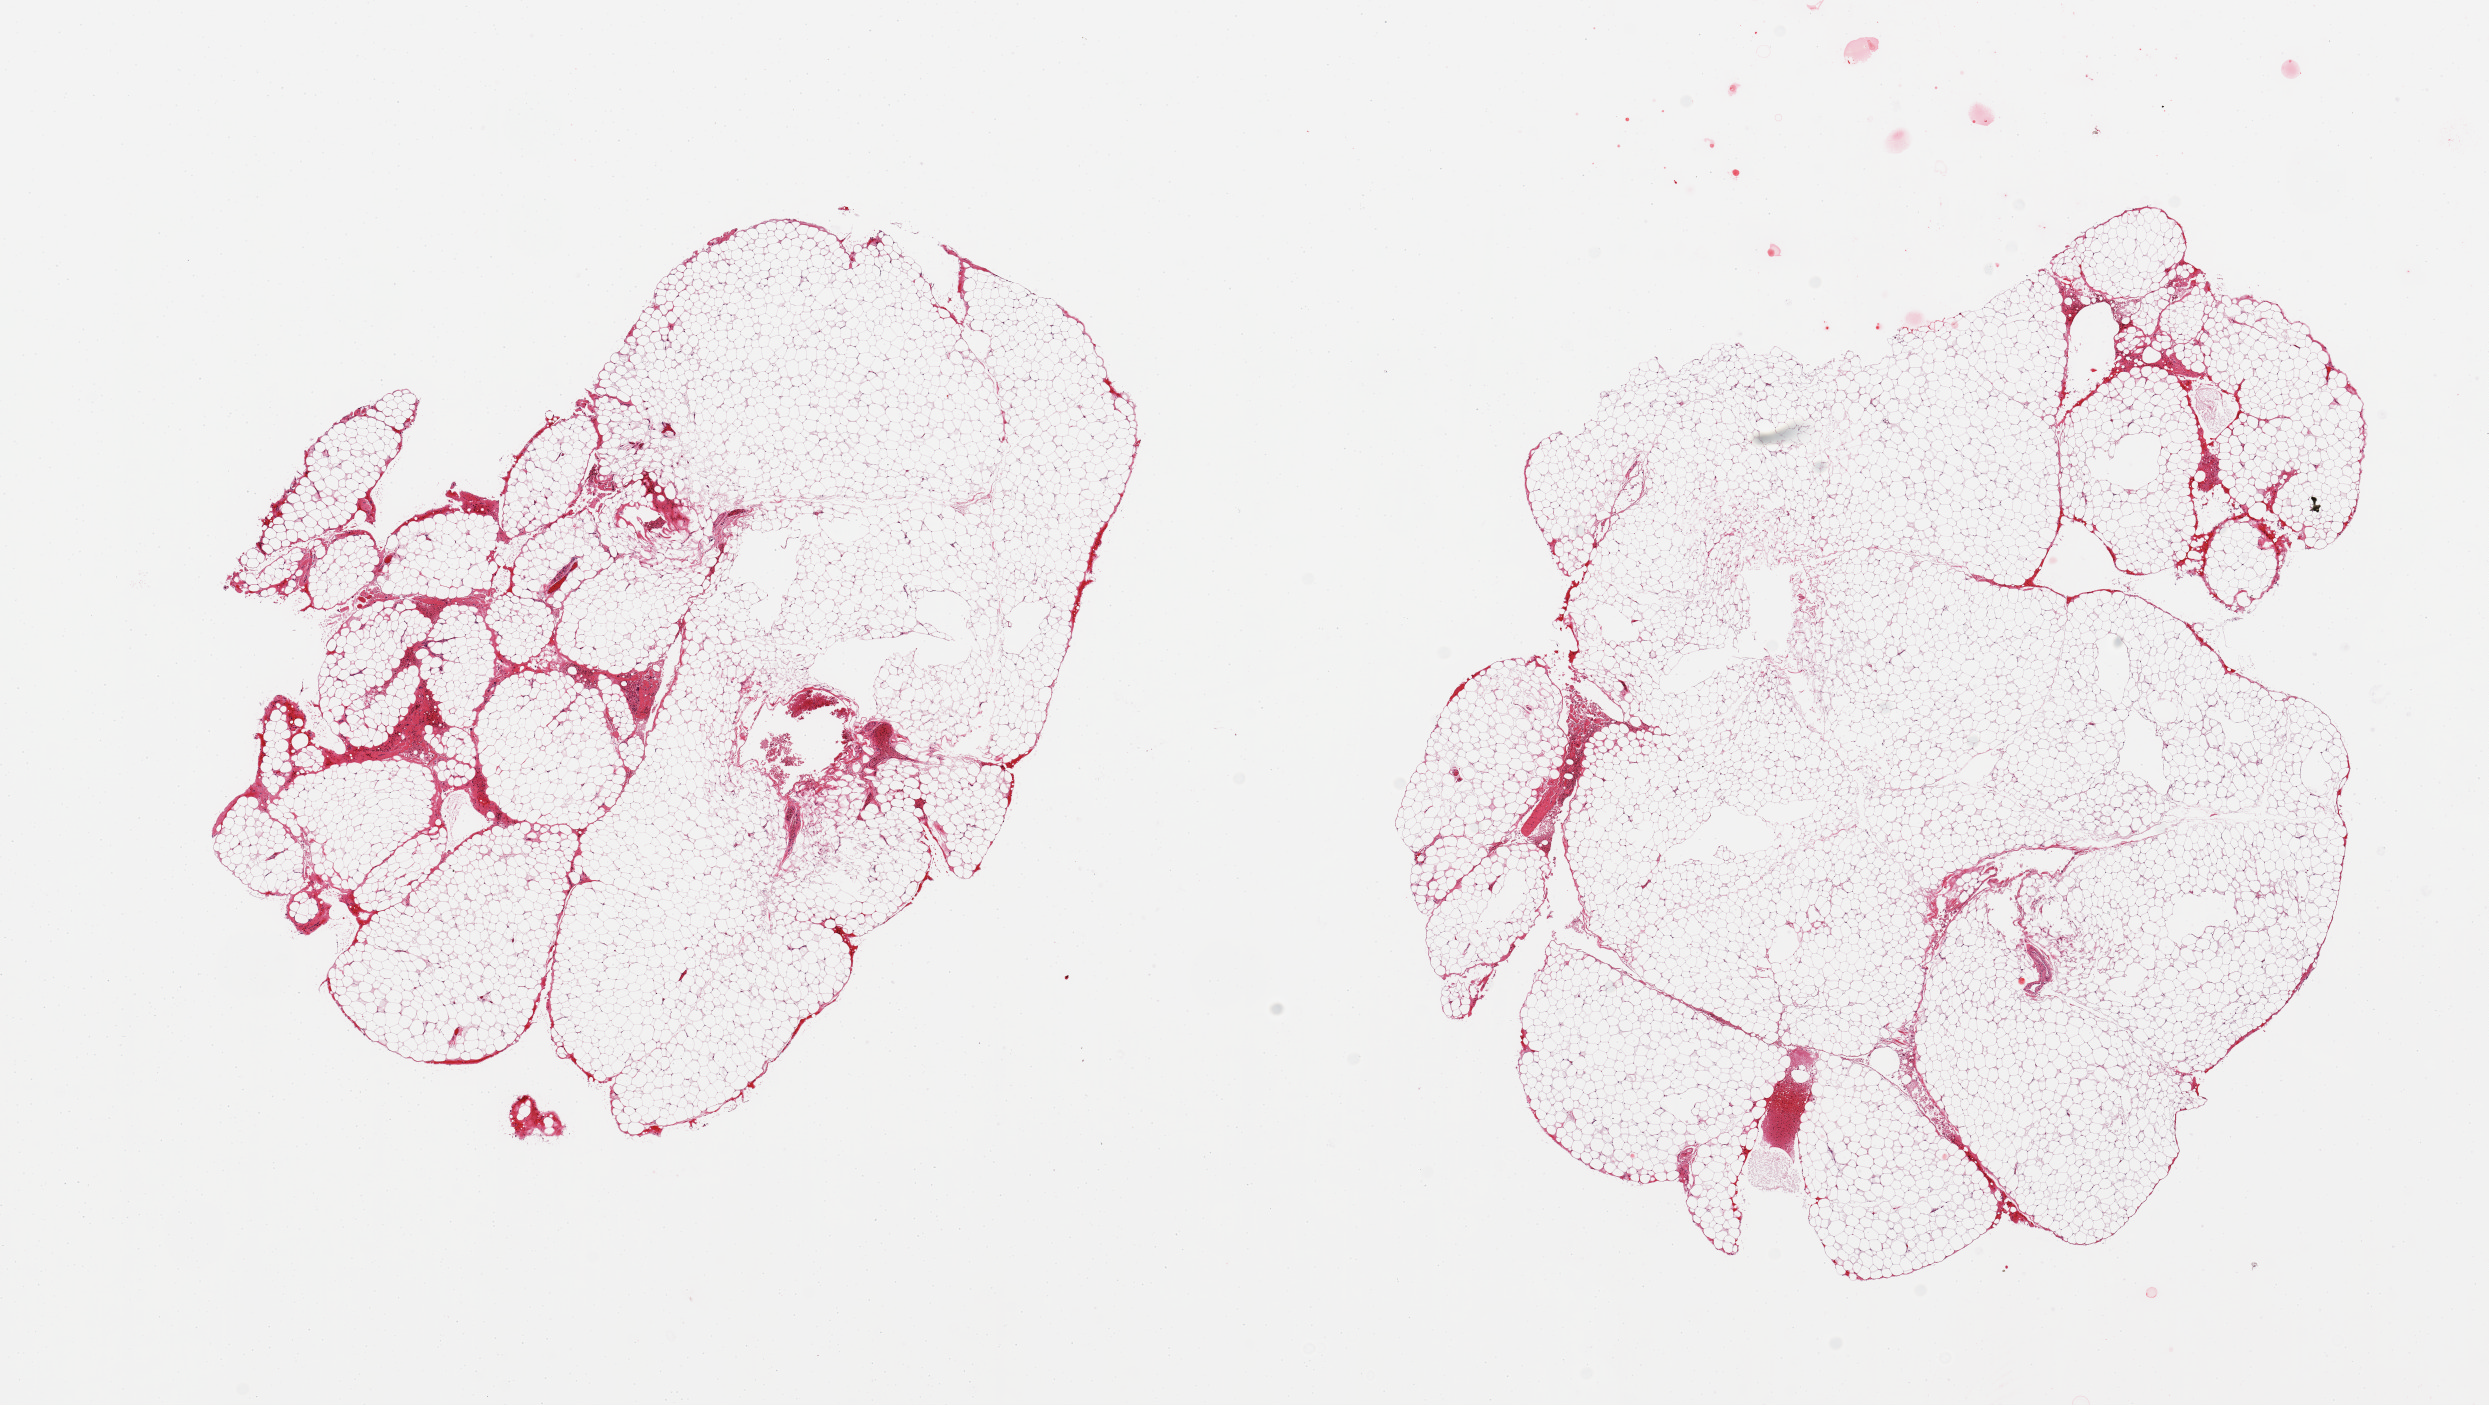
H&E whole-slide image, low-resolution overview of the scanned area, about 19.7 x 11.1 mm (acquisition: 20x scan). PAXgene-fixed paraffin-embedded (PFPE) section. Section of omentum (target tissue). Tissue donor sample.
Pathologist's review note for this sample: 2 pieces, ~10% interstitial fascia/vascular elements.